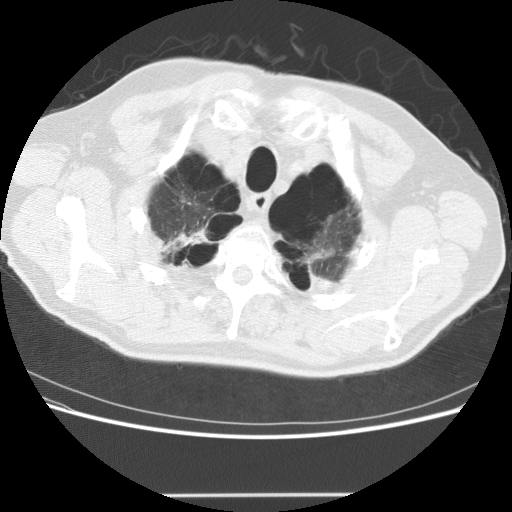
Low-dose screening chest CT, axial slice; third annual screen; lung window (W 1500 / L -600 HU); 120 kVp; 512 × 512 image matrix. Male, age 68 years at enrolment. Former smoker at enrolment.
Lesion marked by an expert reader, bounding box <134,211,219,280> (left, top, right, bottom; pixels). The screening reader recorded 2 non-calcified nodules or masses ≥4 mm on this exam (lingula, left lower lobe); which of them this box marks is not recorded. Later outcome: lung cancer diagnosed 301 days after this screen — large cell carcinoma, NOS, right upper lobe, poorly differentiated (G3), stage IV (AJCC 6th edition).